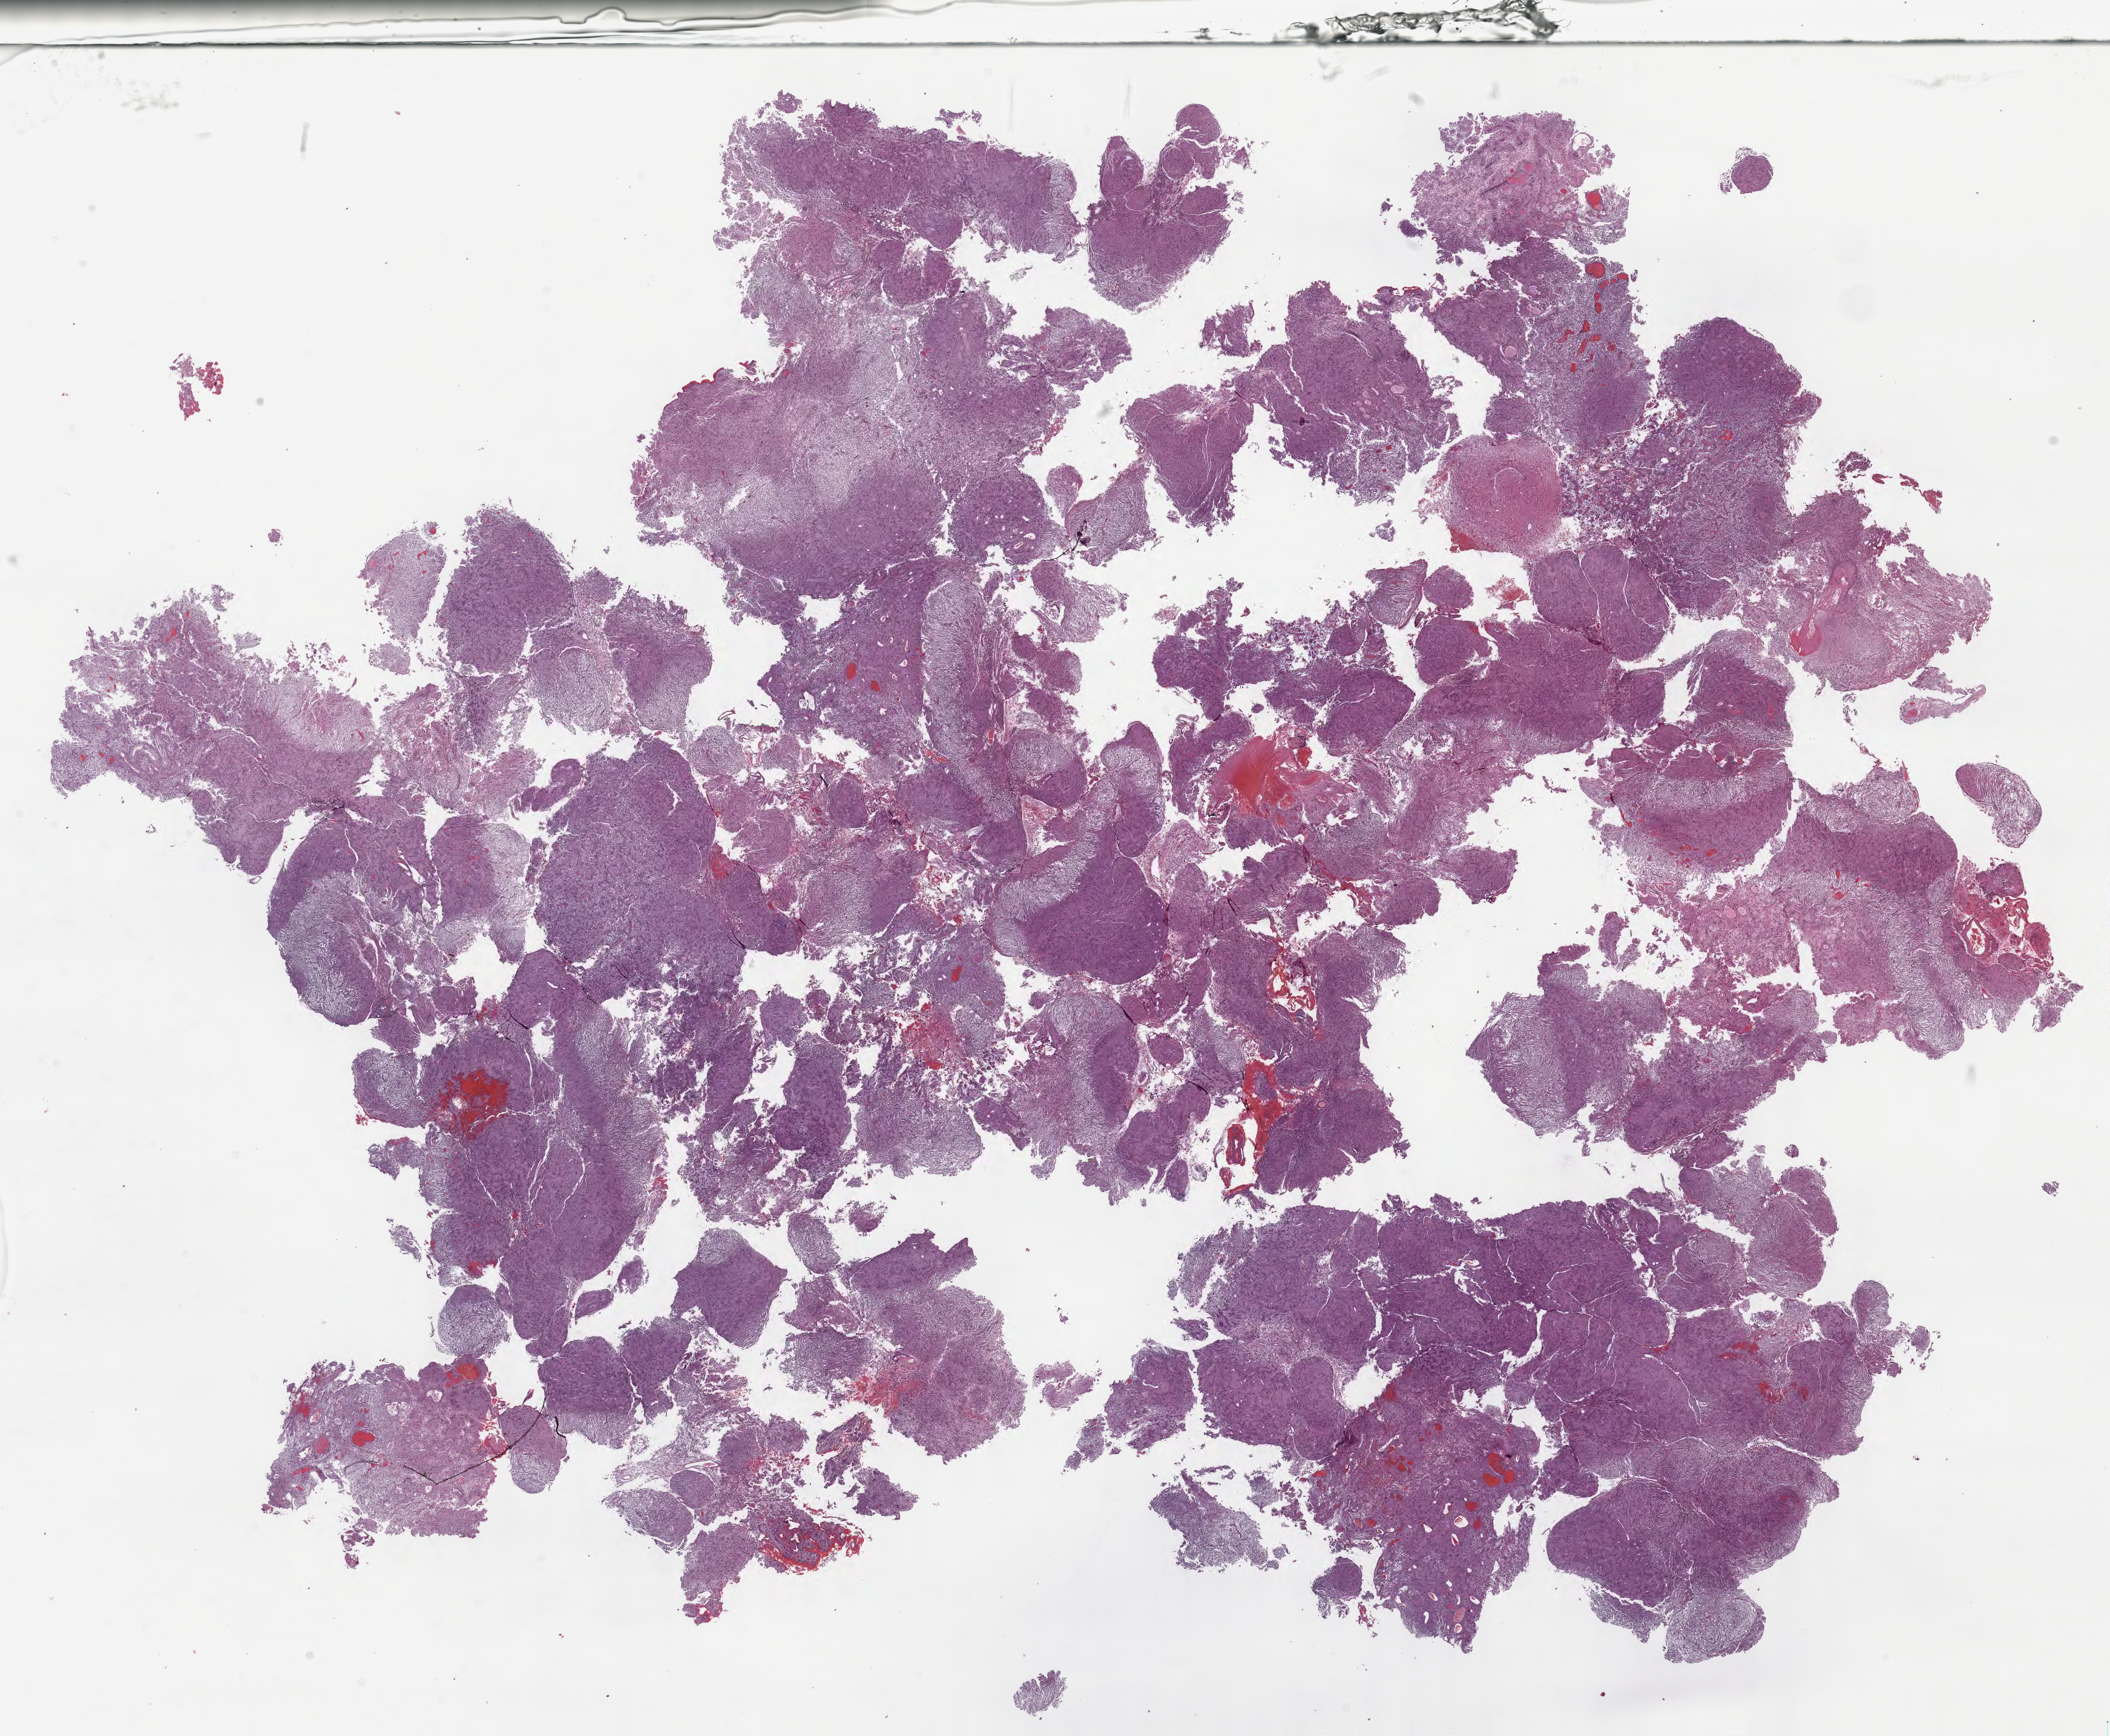
Digitized haematoxylin and eosin-stained section of tumor tissue from the brain — shown as a low-resolution overview of the whole scanned area (about 28.2 x 23.2 mm); formalin-fixed, paraffin-embedded (FFPE) tissue. Patient male; age 196 months (16 years 4 months).
Diagnosis: Neoplasm, malignant.